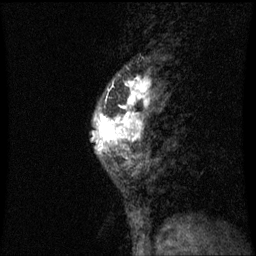
Breast MRI (dynamic contrast-enhanced), one sagittal slice; position 23 of 60 along the scan axis; dynamic contrast-enhanced series, image 2 of 3 at this slice position (ordered by acquisition); 1.5 T; TE 4.2 ms, TR 8.9 ms; 2 mm slice thickness; 256 × 256 image matrix. Patient: female, 50 years. Case-level facts recorded for this patient, not image findings: setting: breast cancer imaged before/during neoadjuvant chemotherapy; receptor status: triple-negative.
Annotated regions visible in this slice (semi-automatically segmented with operator editing):
- analysis volume of interest (the breast-tissue region the enhancement analysis was run in; not a lesion): bounding box (x1, y1, x2, y2) in pixels: (92, 80, 157, 171)
- tumour enhancement mask (voxels above the 70 % enhancement threshold inside the analysis volume of interest): (96, 80, 151, 149)